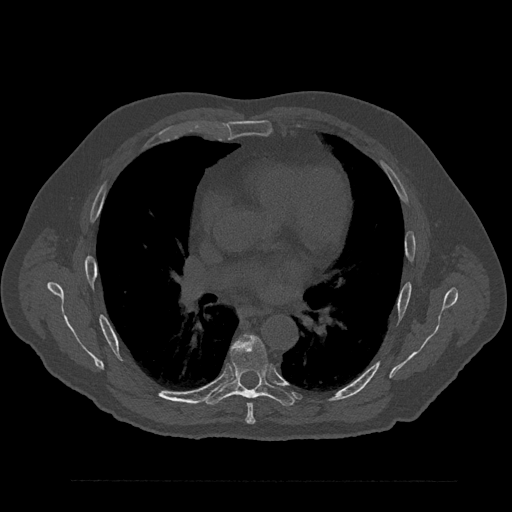
CT including the spine, one axial slice; slice 521 of 797 in the series (ordered by position); bone window (W 1800 / L 400 HU); 0.5 mm slice thickness; 512 × 512 image matrix, field of view 430 × 430 mm. Patient: male, 61 years. From the clinical record (not read from this slice): primary cancer: prostate.
Structures marked on this image (semi-automatic segmentation, software-assisted and operator-edited):
- T6 vertebra: bounding box <246,403,256,424> (left, top, right, bottom; pixels)
- T7 vertebra: <204,335,295,406>